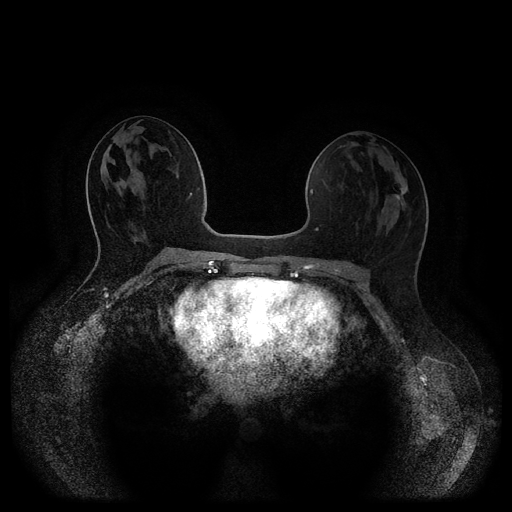
Breast MRI (dynamic contrast-enhanced, multi-phase), one axial slice; position 50 of 116 along the scan axis; dynamic contrast-enhanced series, time point 2 of 5 at this slice position (early post-contrast); 1.5 T; TE 2.6 ms, TR 5.3 ms; 512 × 512 image matrix, field of view 360 × 360 mm. Patient: female, 27 years.
Structures marked on this image (semi-automatically segmented with operator editing):
- breast lesion (labelled 'tumour' in the annotation; benign lesions carry a separate 'benign' label): bounding box (x1, y1, x2, y2) in pixels: (396, 187, 407, 205)